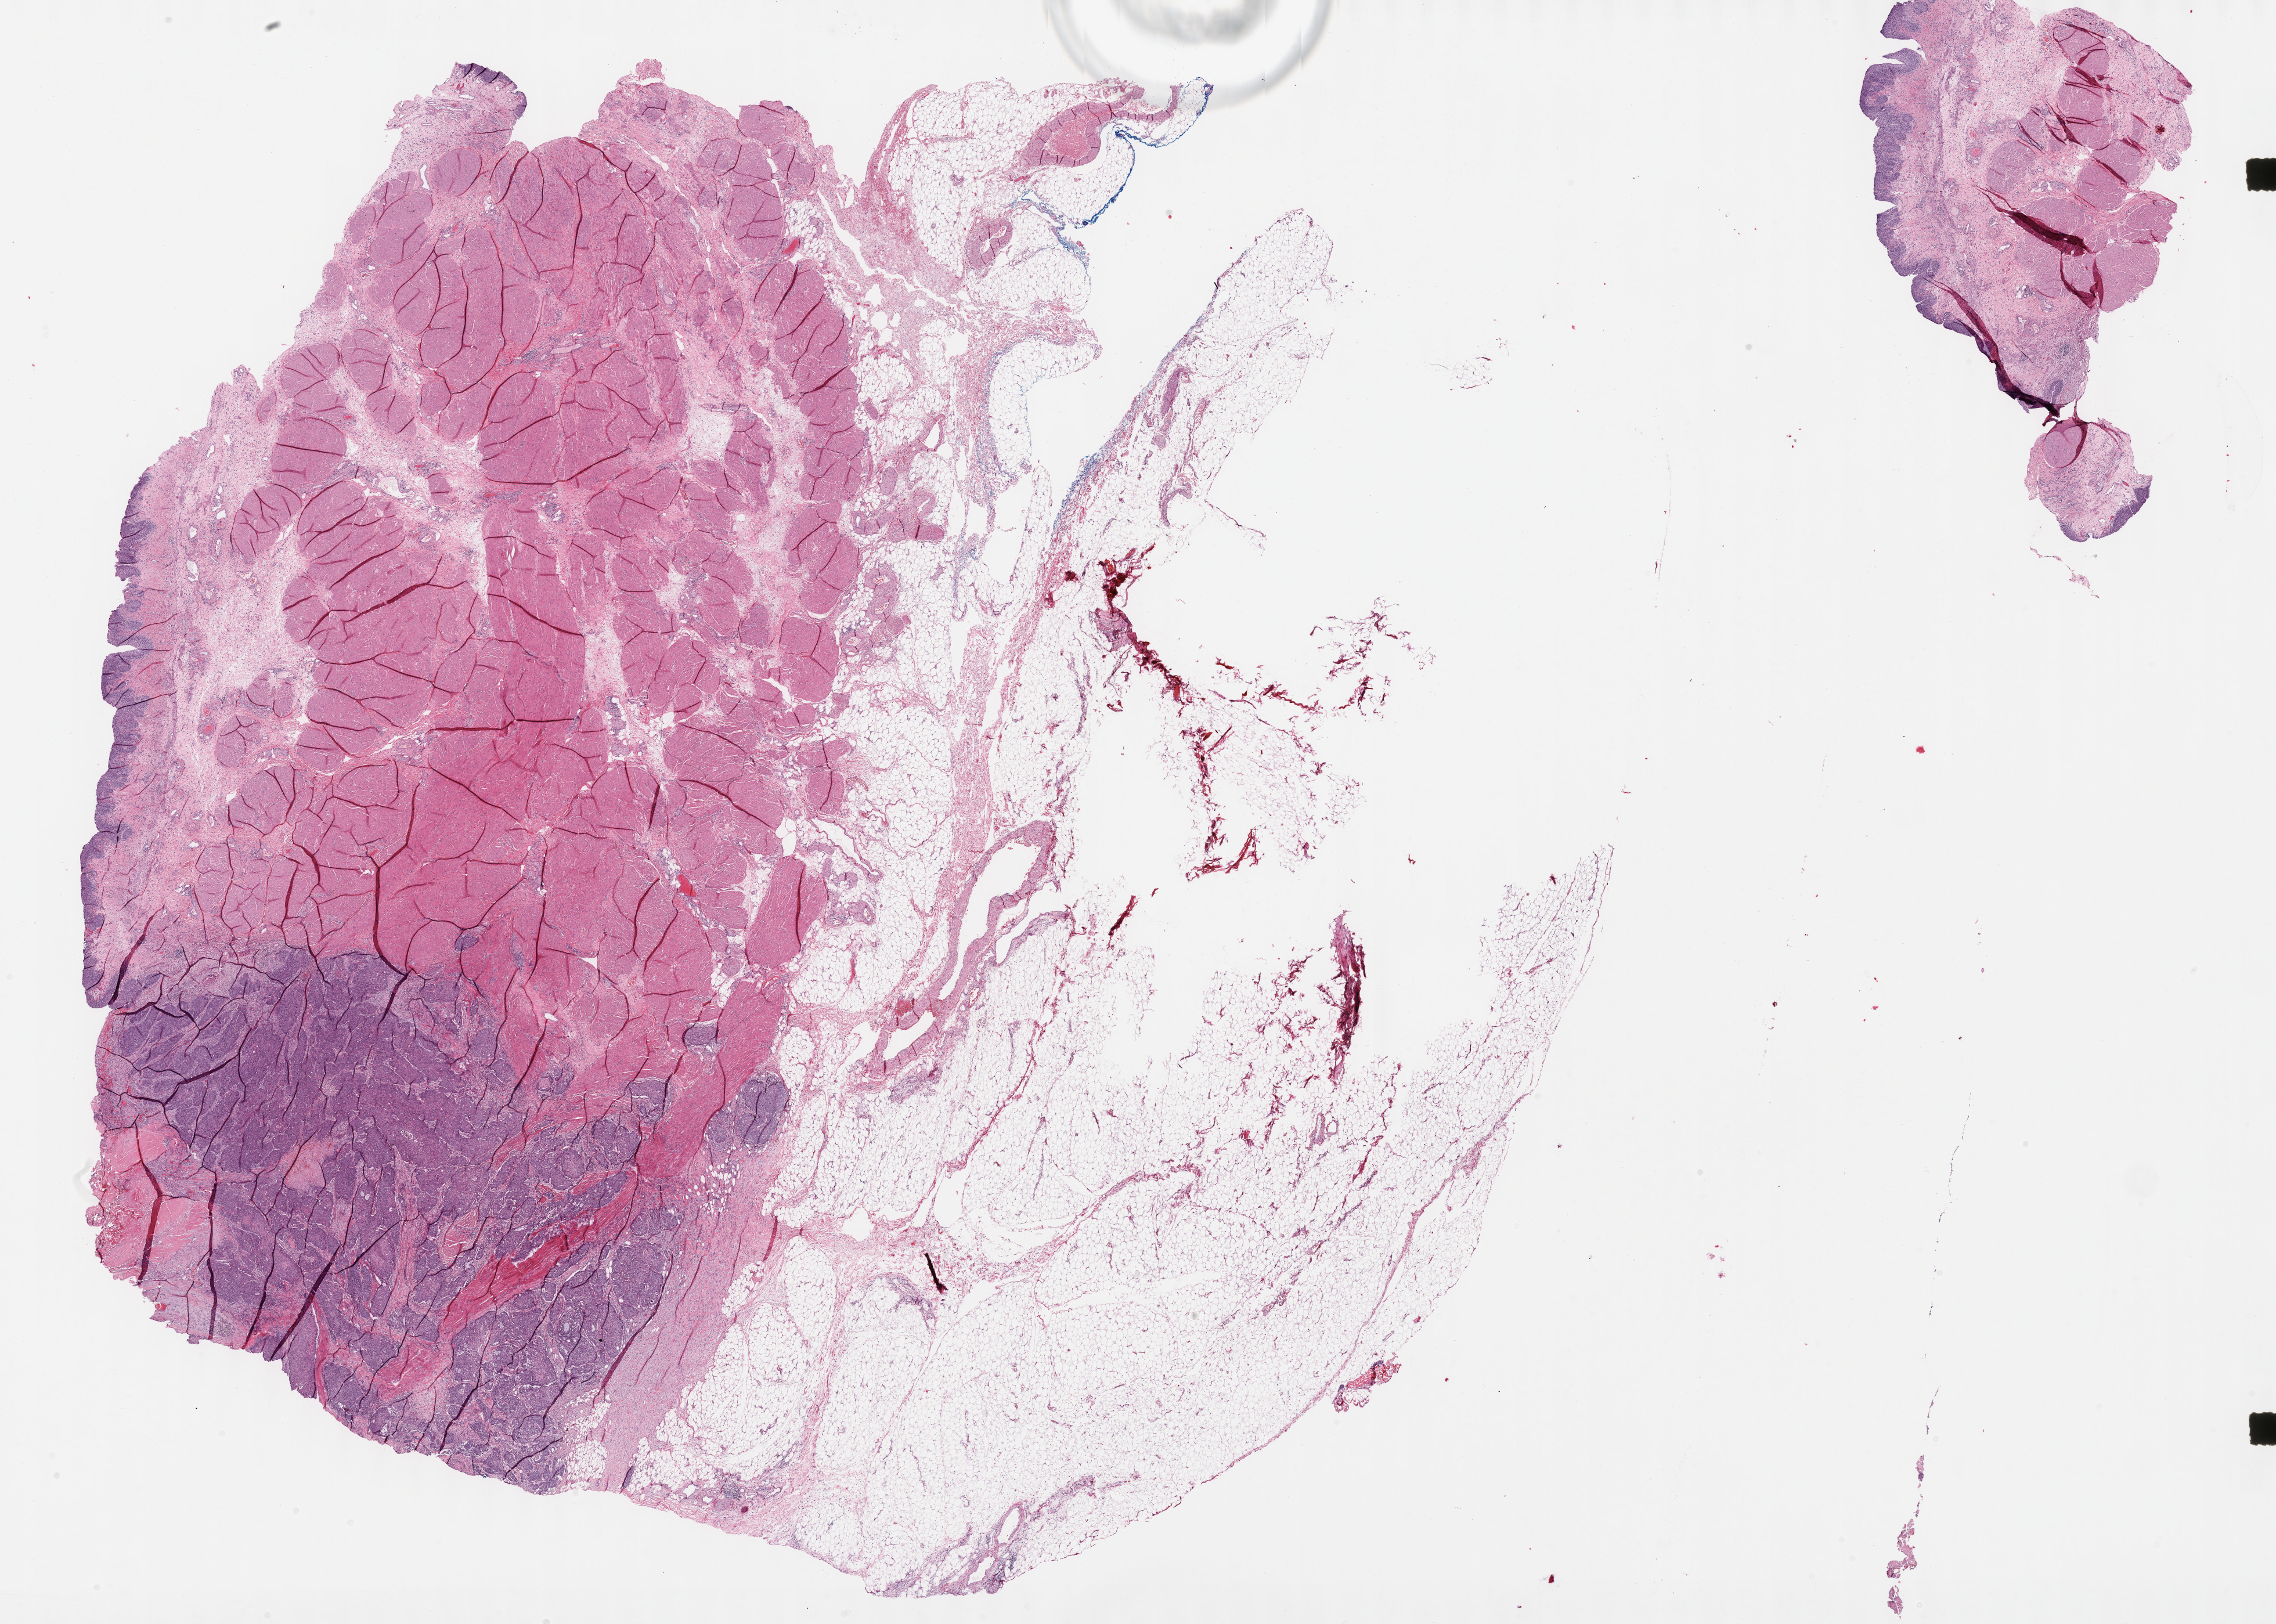
Whole-slide histology image, Hematoxylin and eosin (H&E) stained, whole scanned area (about 31.7 x 22.6 mm, acquisition: 40x scan) shown as a low-resolution overview; FFPE section; primary tumour sample from the bladder. Patient: male, age at initial diagnosis 68 years. Histologic grade: high grade.
Lymph nodes positive (case pathology): 0 of 21 examined. Diagnosis: Transitional cell carcinoma. AJCC pathologic stage: III (7th edition).